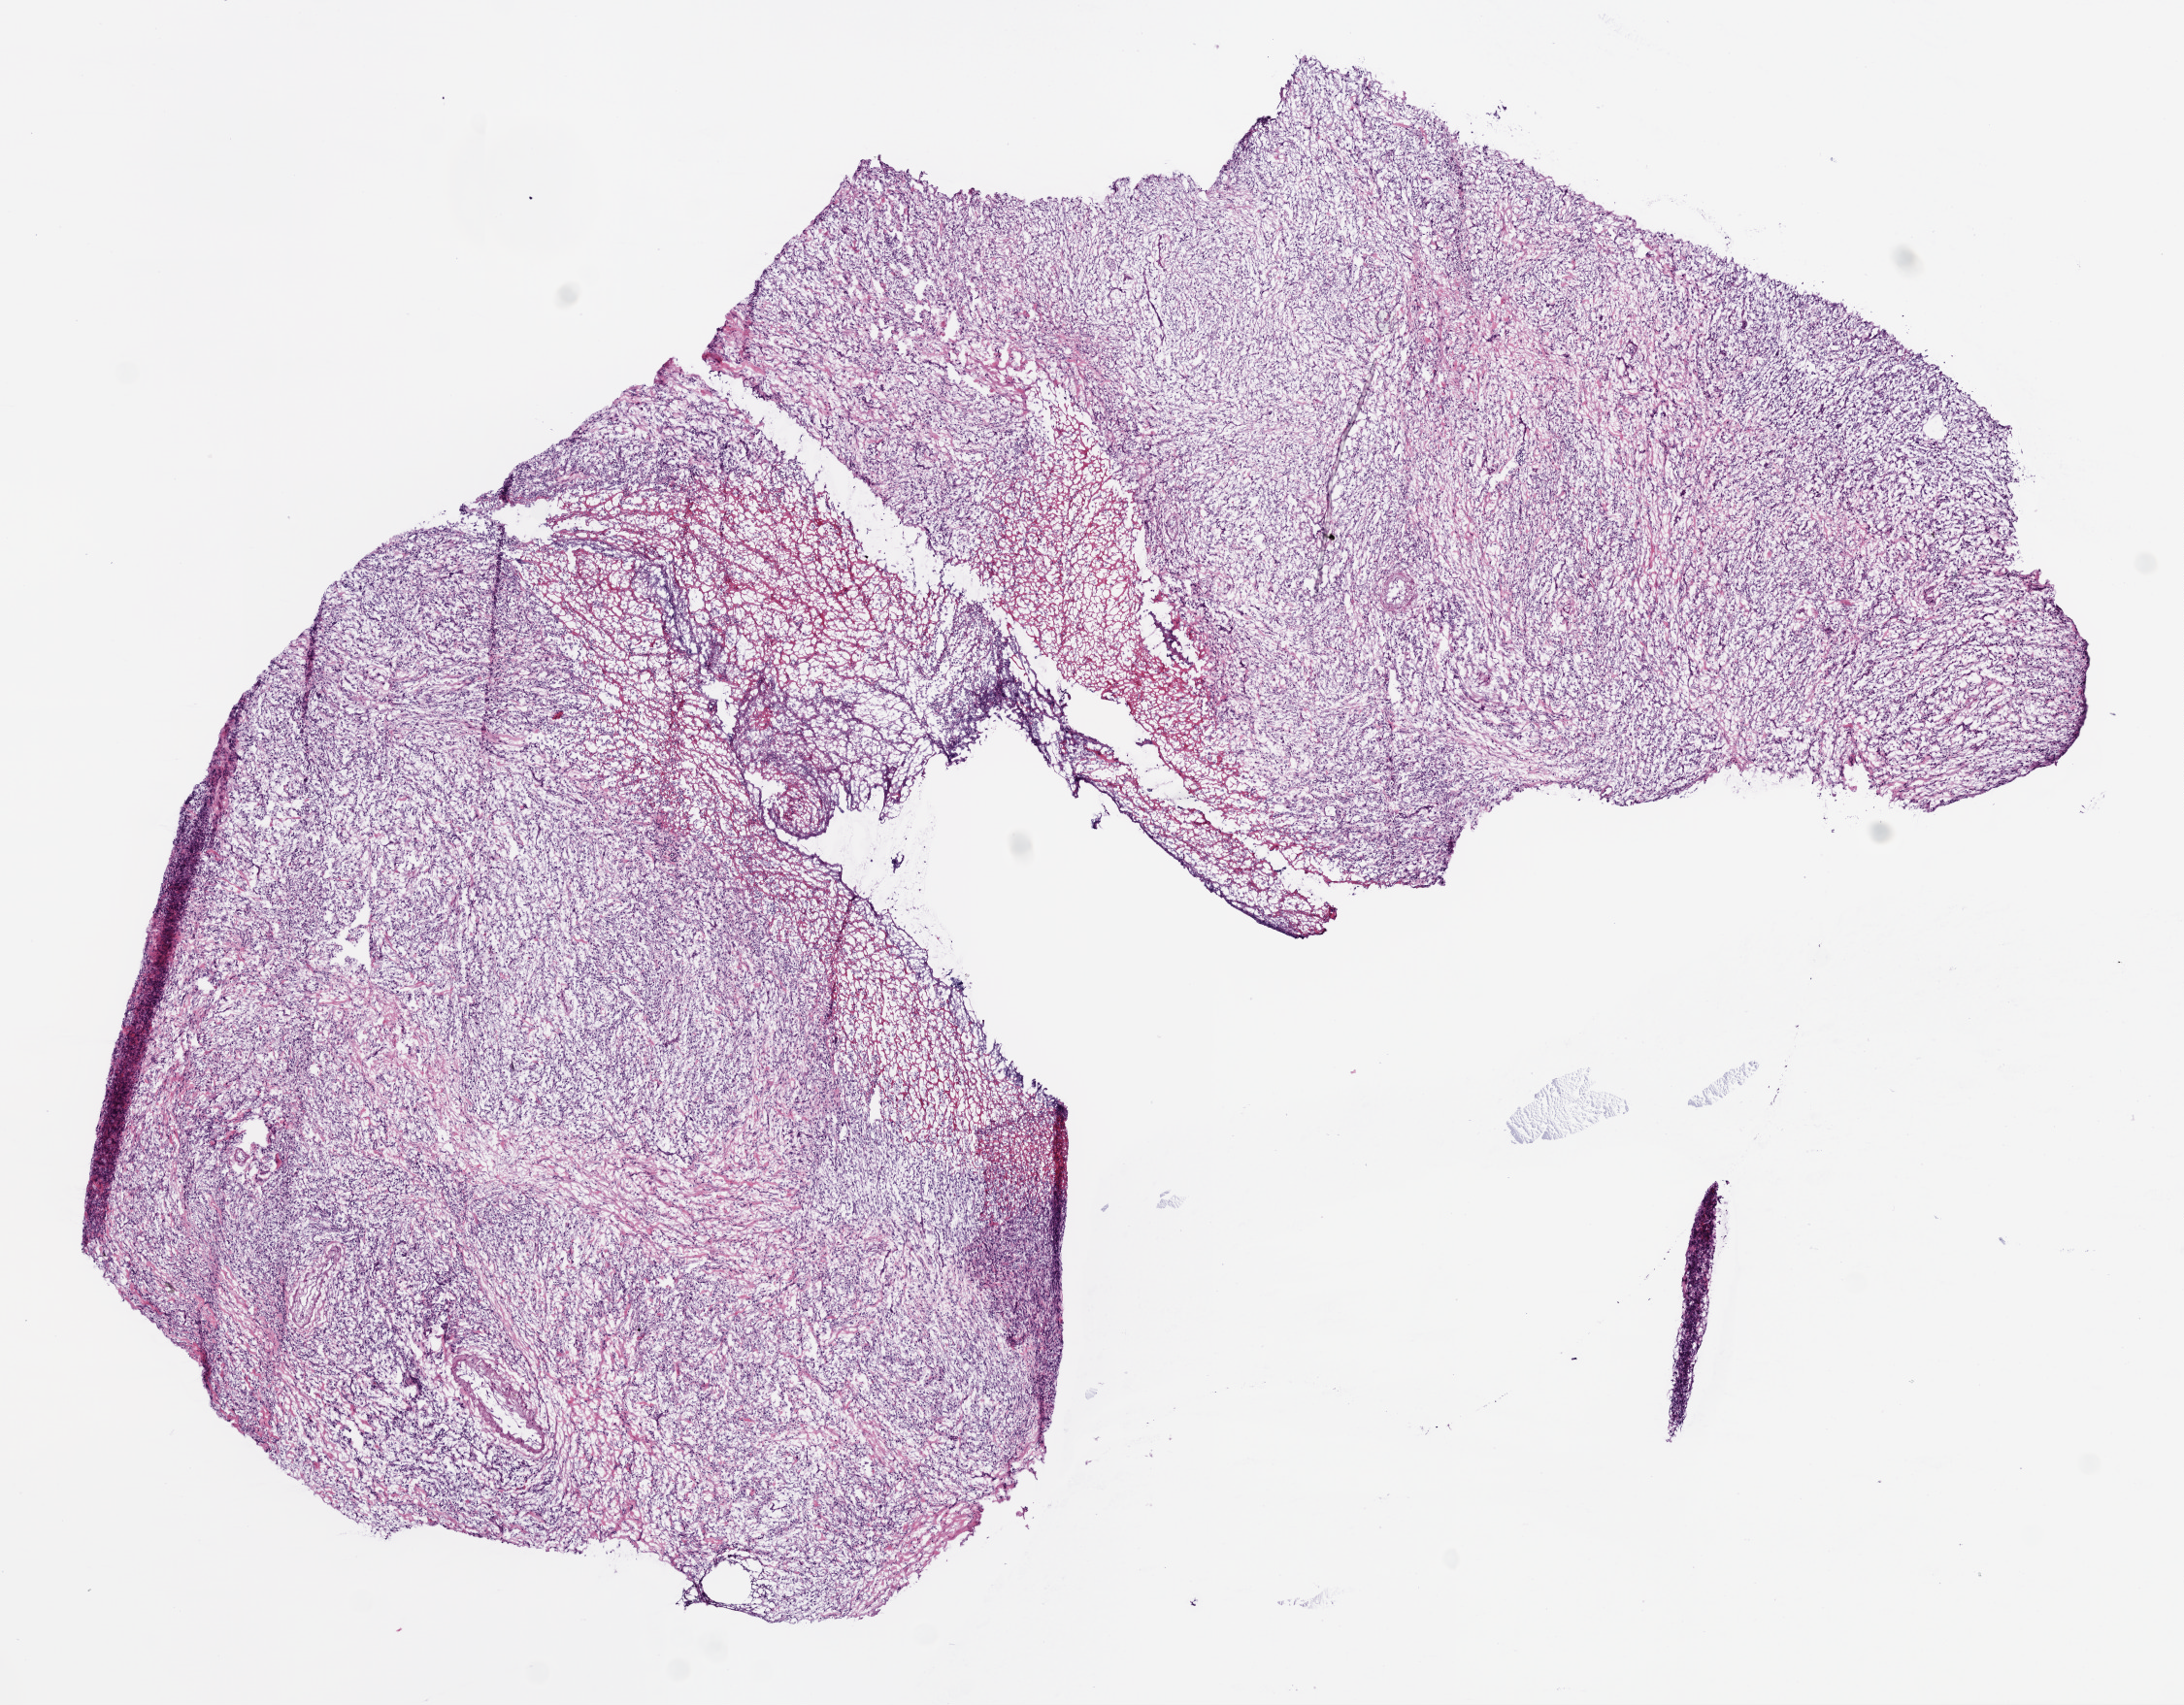
Whole-slide histology image, H&E, whole scanned area (about 9.0 x 7.0 mm, acquisition: 20x scan) shown as a low-resolution overview, frozen section from the bottom of the tissue portion, stomach, primary tumour sample. Patient: female, age at initial diagnosis 72 years.
Histologic diagnosis: Carcinoma, diffuse type.